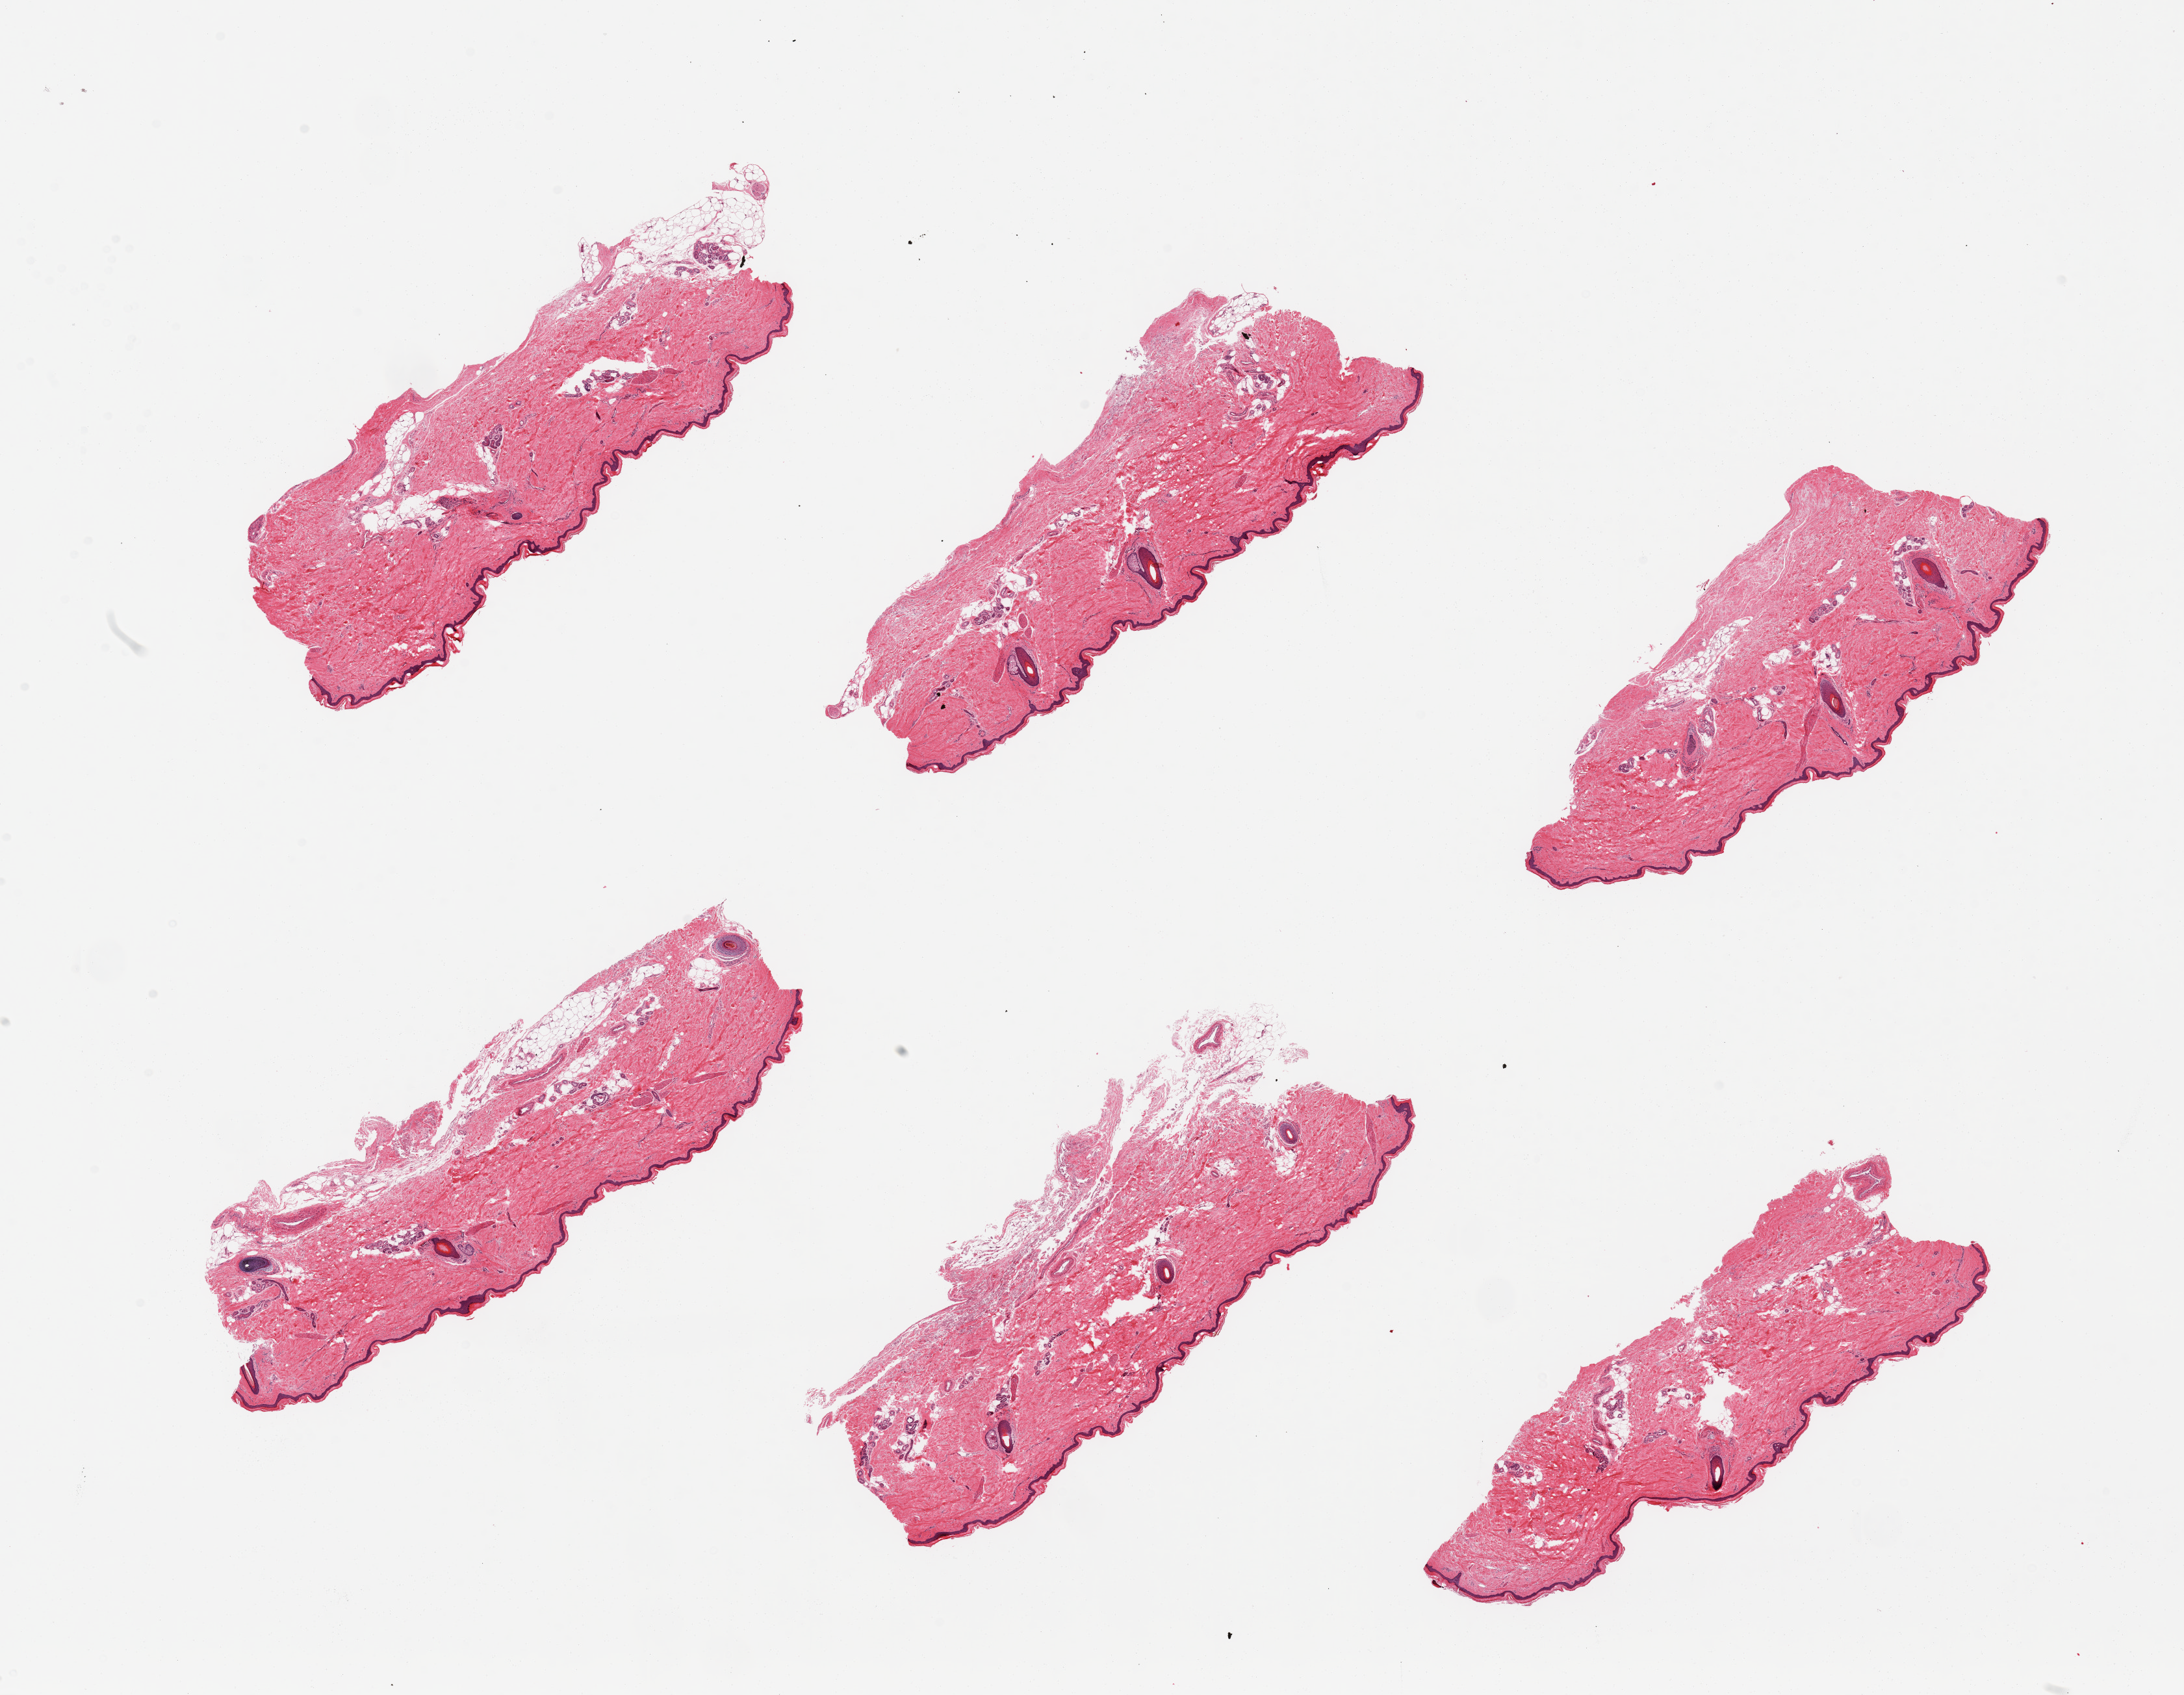
Digitized hematoxylin and eosin (H&E)-stained section, a low-resolution overview of the entire scanned area, about 26.6 x 20.6 mm (acquisition: 20x scan), PAXgene-fixed paraffin-embedded (PFPE) section, sampled site (target tissue): skin of lower leg, tissue donor sample. Male donor.
Pathologist's review note for this sample: 6 pieces, minimal dermal fat; squamous epithelium is 30-50 microns.